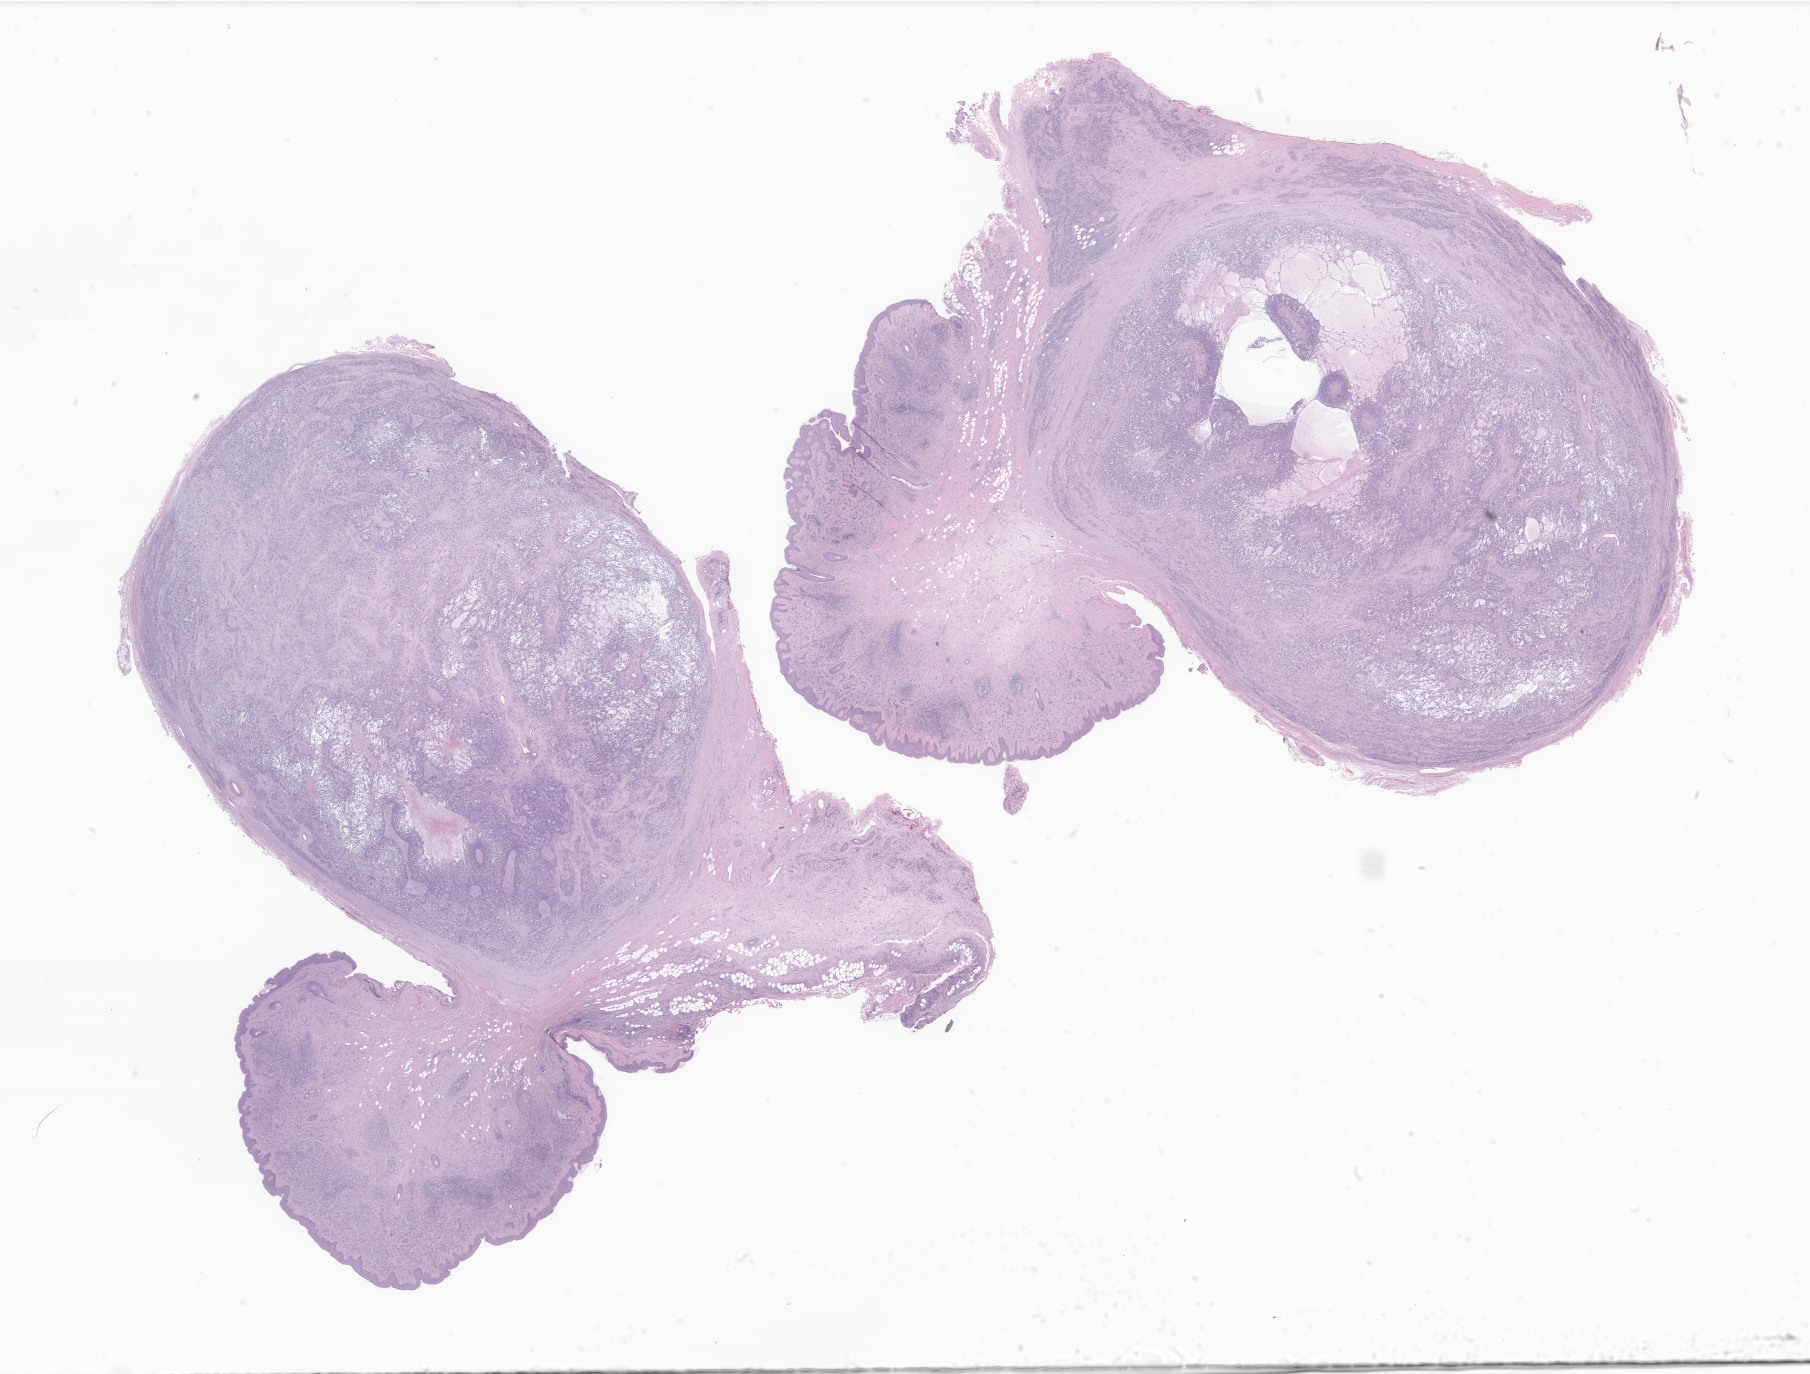
H&E whole-slide image of tumor tissue from the external ear, whole scanned area (about 30.5 x 23.2 mm) shown as a low-resolution overview. Formalin-fixed, paraffin-embedded (FFPE) tissue. Patient male; age 88 months.
Recorded diagnosis: Rhabdomyosarcoma, NOS.